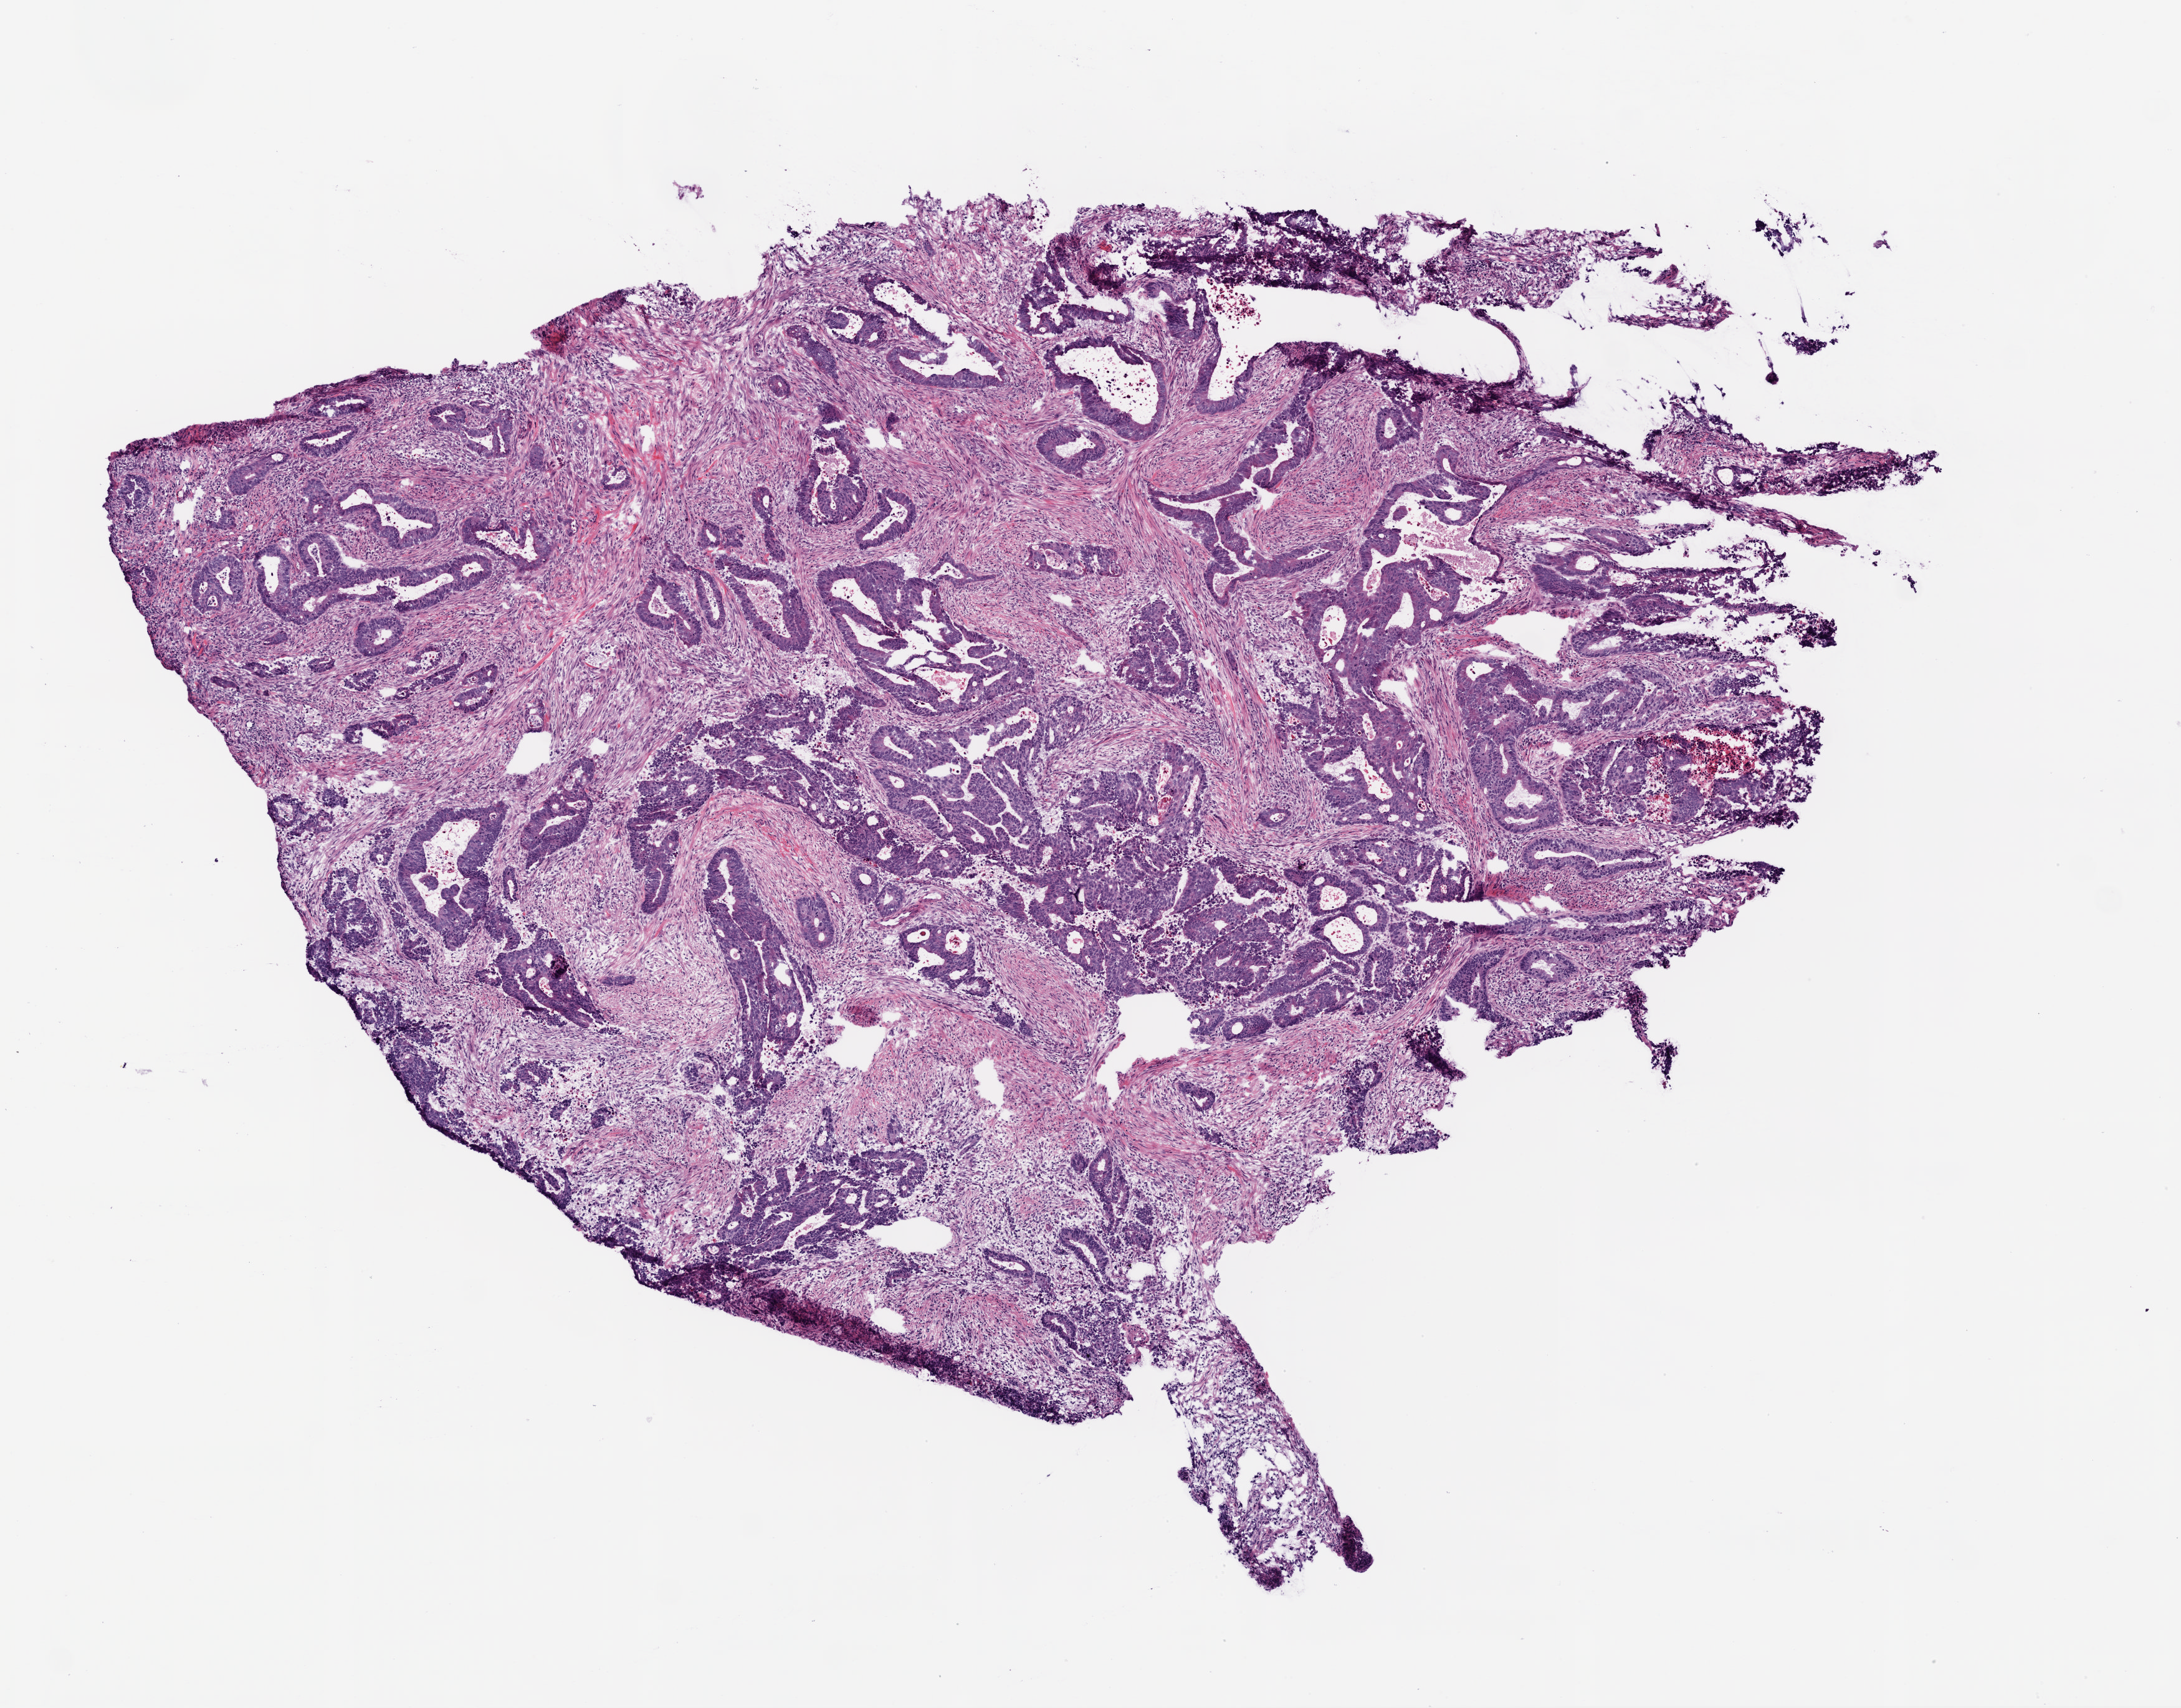
Digitized H&E-stained tissue section (whole slide) — shown as a low-resolution overview of the whole scanned area (about 7.0 x 5.5 mm). Frozen section from the top of the tissue portion. Rectum, primary tumour sample. Male, age 83 years at initial diagnosis. Pathologist review of this section (percent, as recorded): tumour cells 67%, tumour nuclei 75%, normal cells 0%, stromal cells 30%, necrosis 3%.
AJCC pathologic stage: I (6th edition). Diagnosis: Adenocarcinoma, NOS. Lymph nodes positive (case pathology): 0 of 16 examined.